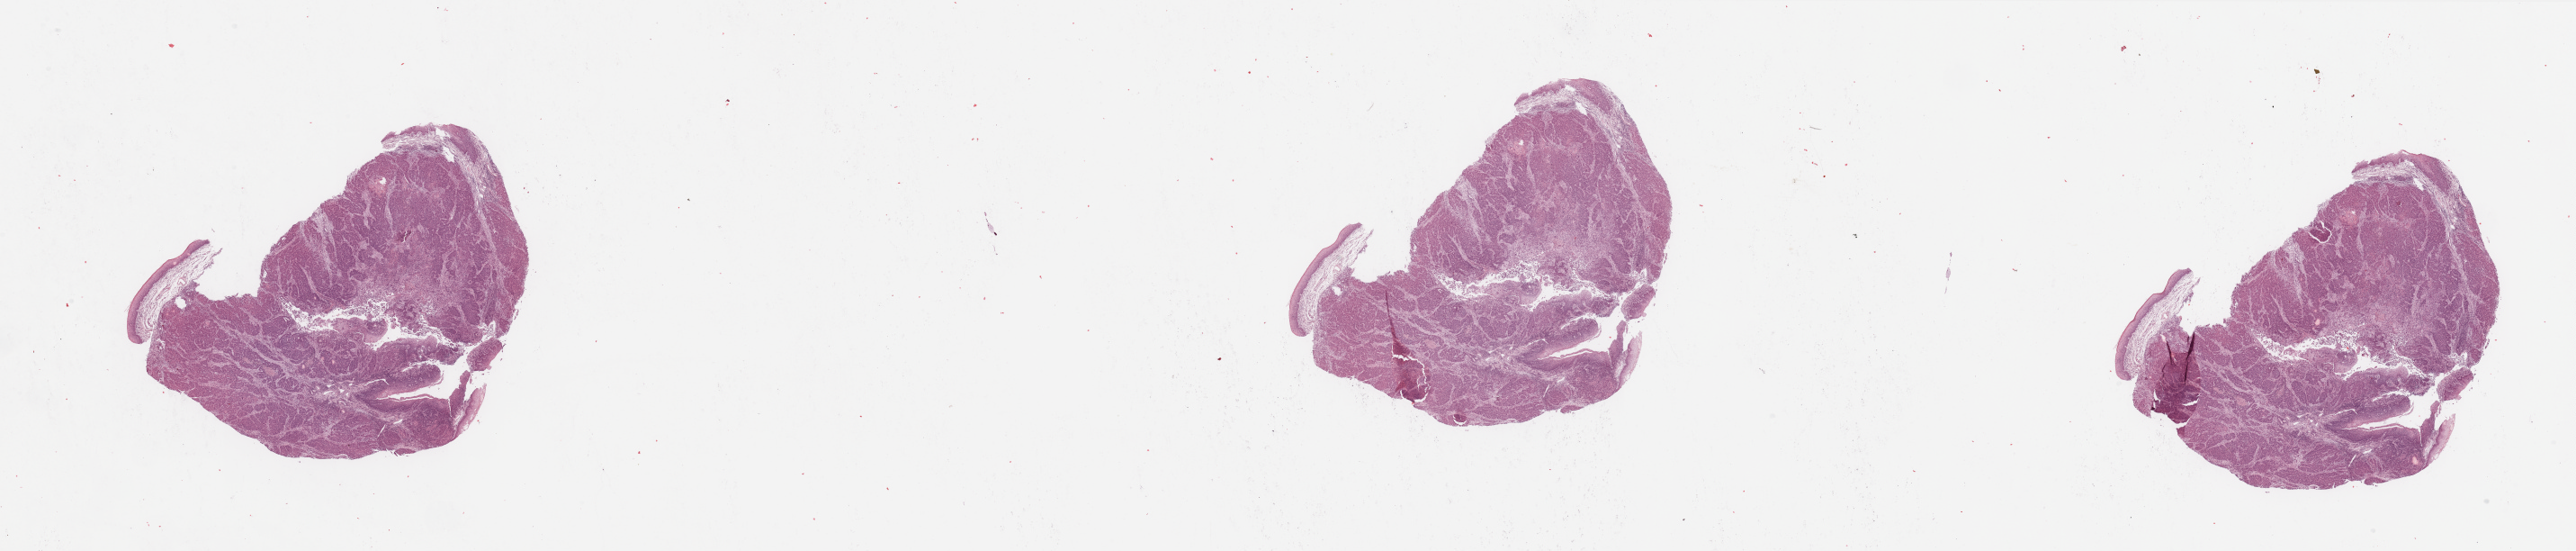
Whole-slide histology image, Hematoxylin and eosin (H&E) stained, a low-resolution overview of the entire scanned area, about 45.3 x 9.7 mm (from a 20x scan); tumour tissue sample, sampled site: larynx. Patient: male, age 71 years. Histologic grade: G2 (moderately differentiated). Slide review estimates, as recorded: tumour nuclei 85%, necrosis 5%.
Primary tumour site (as recorded): larynx. Histologic diagnosis: Squamous cell carcinoma, NOS (larynx, NOS). AJCC pathologic stage: III.